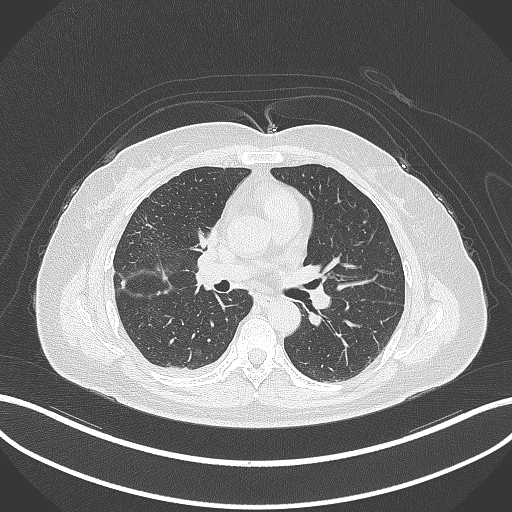
Chest CT, one axial slice; slice 149 of 305 in the series (ordered by position); 120 kVp; lung window (W 1500 / L -600 HU); 1 mm slice thickness; 512 × 512 image matrix. Patient: female, 52 years. From the clinical record (not read from this slice): clinical TNM (as recorded): T3 N1 M1.
Structures marked on this image (bounding box drawn by a radiologist):
- lung tumour (recorded histology: adenocarcinoma): box from (x=188, y=212) to (x=208, y=252) px